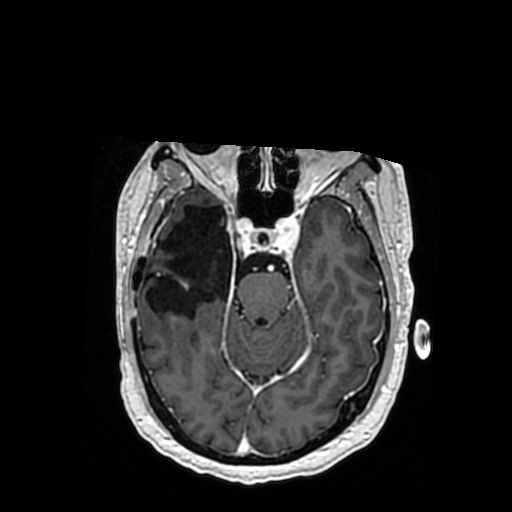
Brain MRI from a brain-tumour surgery series, one axial slice. T1-weighted post-contrast. 0.5 mm slice thickness. 512 × 512 image matrix, field of view 260 × 260 mm. From the clinical record (not read from this slice): histopathology: Oligodendroglioma; WHO grade: 3; IDH mutation: yes; tumour location: Right Posterior Temporal Inferior Parietal.
Outlined on this slice (manually delineated by an expert):
- previous resection cavity: bounding box (x1, y1, x2, y2) in pixels: (144, 205, 232, 317)